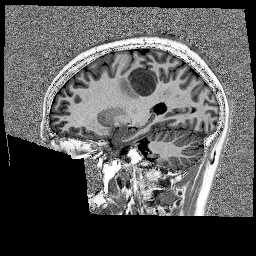
Brain MRI from a brain-tumour surgery series, one sagittal slice; slice 67 of 176 in the series (ordered by position); 256 × 256 image matrix. From the clinical record (not read from this slice): histopathology: Glioblastoma; WHO grade: 4; IDH mutation: no.
Outlined on this slice (manually delineated by an expert):
- tumour: bounding box <118,62,175,92> (left, top, right, bottom; pixels)